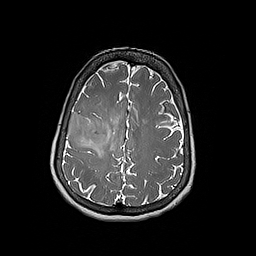
Brain MRI from a brain-tumour surgery series, one axial slice; position 68 of 192 along the scan axis; 256 × 256 image matrix, field of view 250 × 250 mm. From the clinical record (not read from this slice): histopathology: Oligodendroglioma; WHO grade: 3; IDH mutation: yes; tumour location: Right Frontal.
Annotated regions visible in this slice (manually delineated by an expert):
- tumour: bounding box <66,112,109,148> (left, top, right, bottom; pixels)